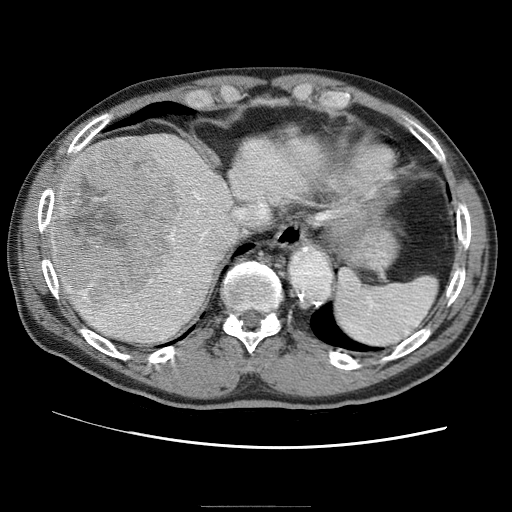
Contrast-enhanced abdominal CT (liver protocol), one axial slice; slice 53 of 75 in the series (ordered by position); 120 kVp; one of 2 acquisitions stored at this slice position; soft-tissue window (W 400 / L 40 HU); 512 × 512 image matrix. Case-level facts recorded for this patient, not image findings: diagnosis: hepatocellular carcinoma (patient treated with transarterial chemoembolisation; whether this scan precedes or follows treatment is not stated here); TNM stage (as recorded): Stage-II; Child-Pugh class: A; tumour differentiation: well differentiated; tumour nodularity: multinodular.
Annotated regions visible in this slice (semi-automatically segmented with operator editing):
- abdominal aorta: bounding box (x1, y1, x2, y2) in pixels: (289, 246, 331, 302)
- liver parenchyma outside the tumour (the mass and vessels are separate outlines, so this box may not span the whole liver): (46, 122, 382, 344)
- mass: (53, 140, 186, 305)
- liver vessels: (48, 185, 367, 323)